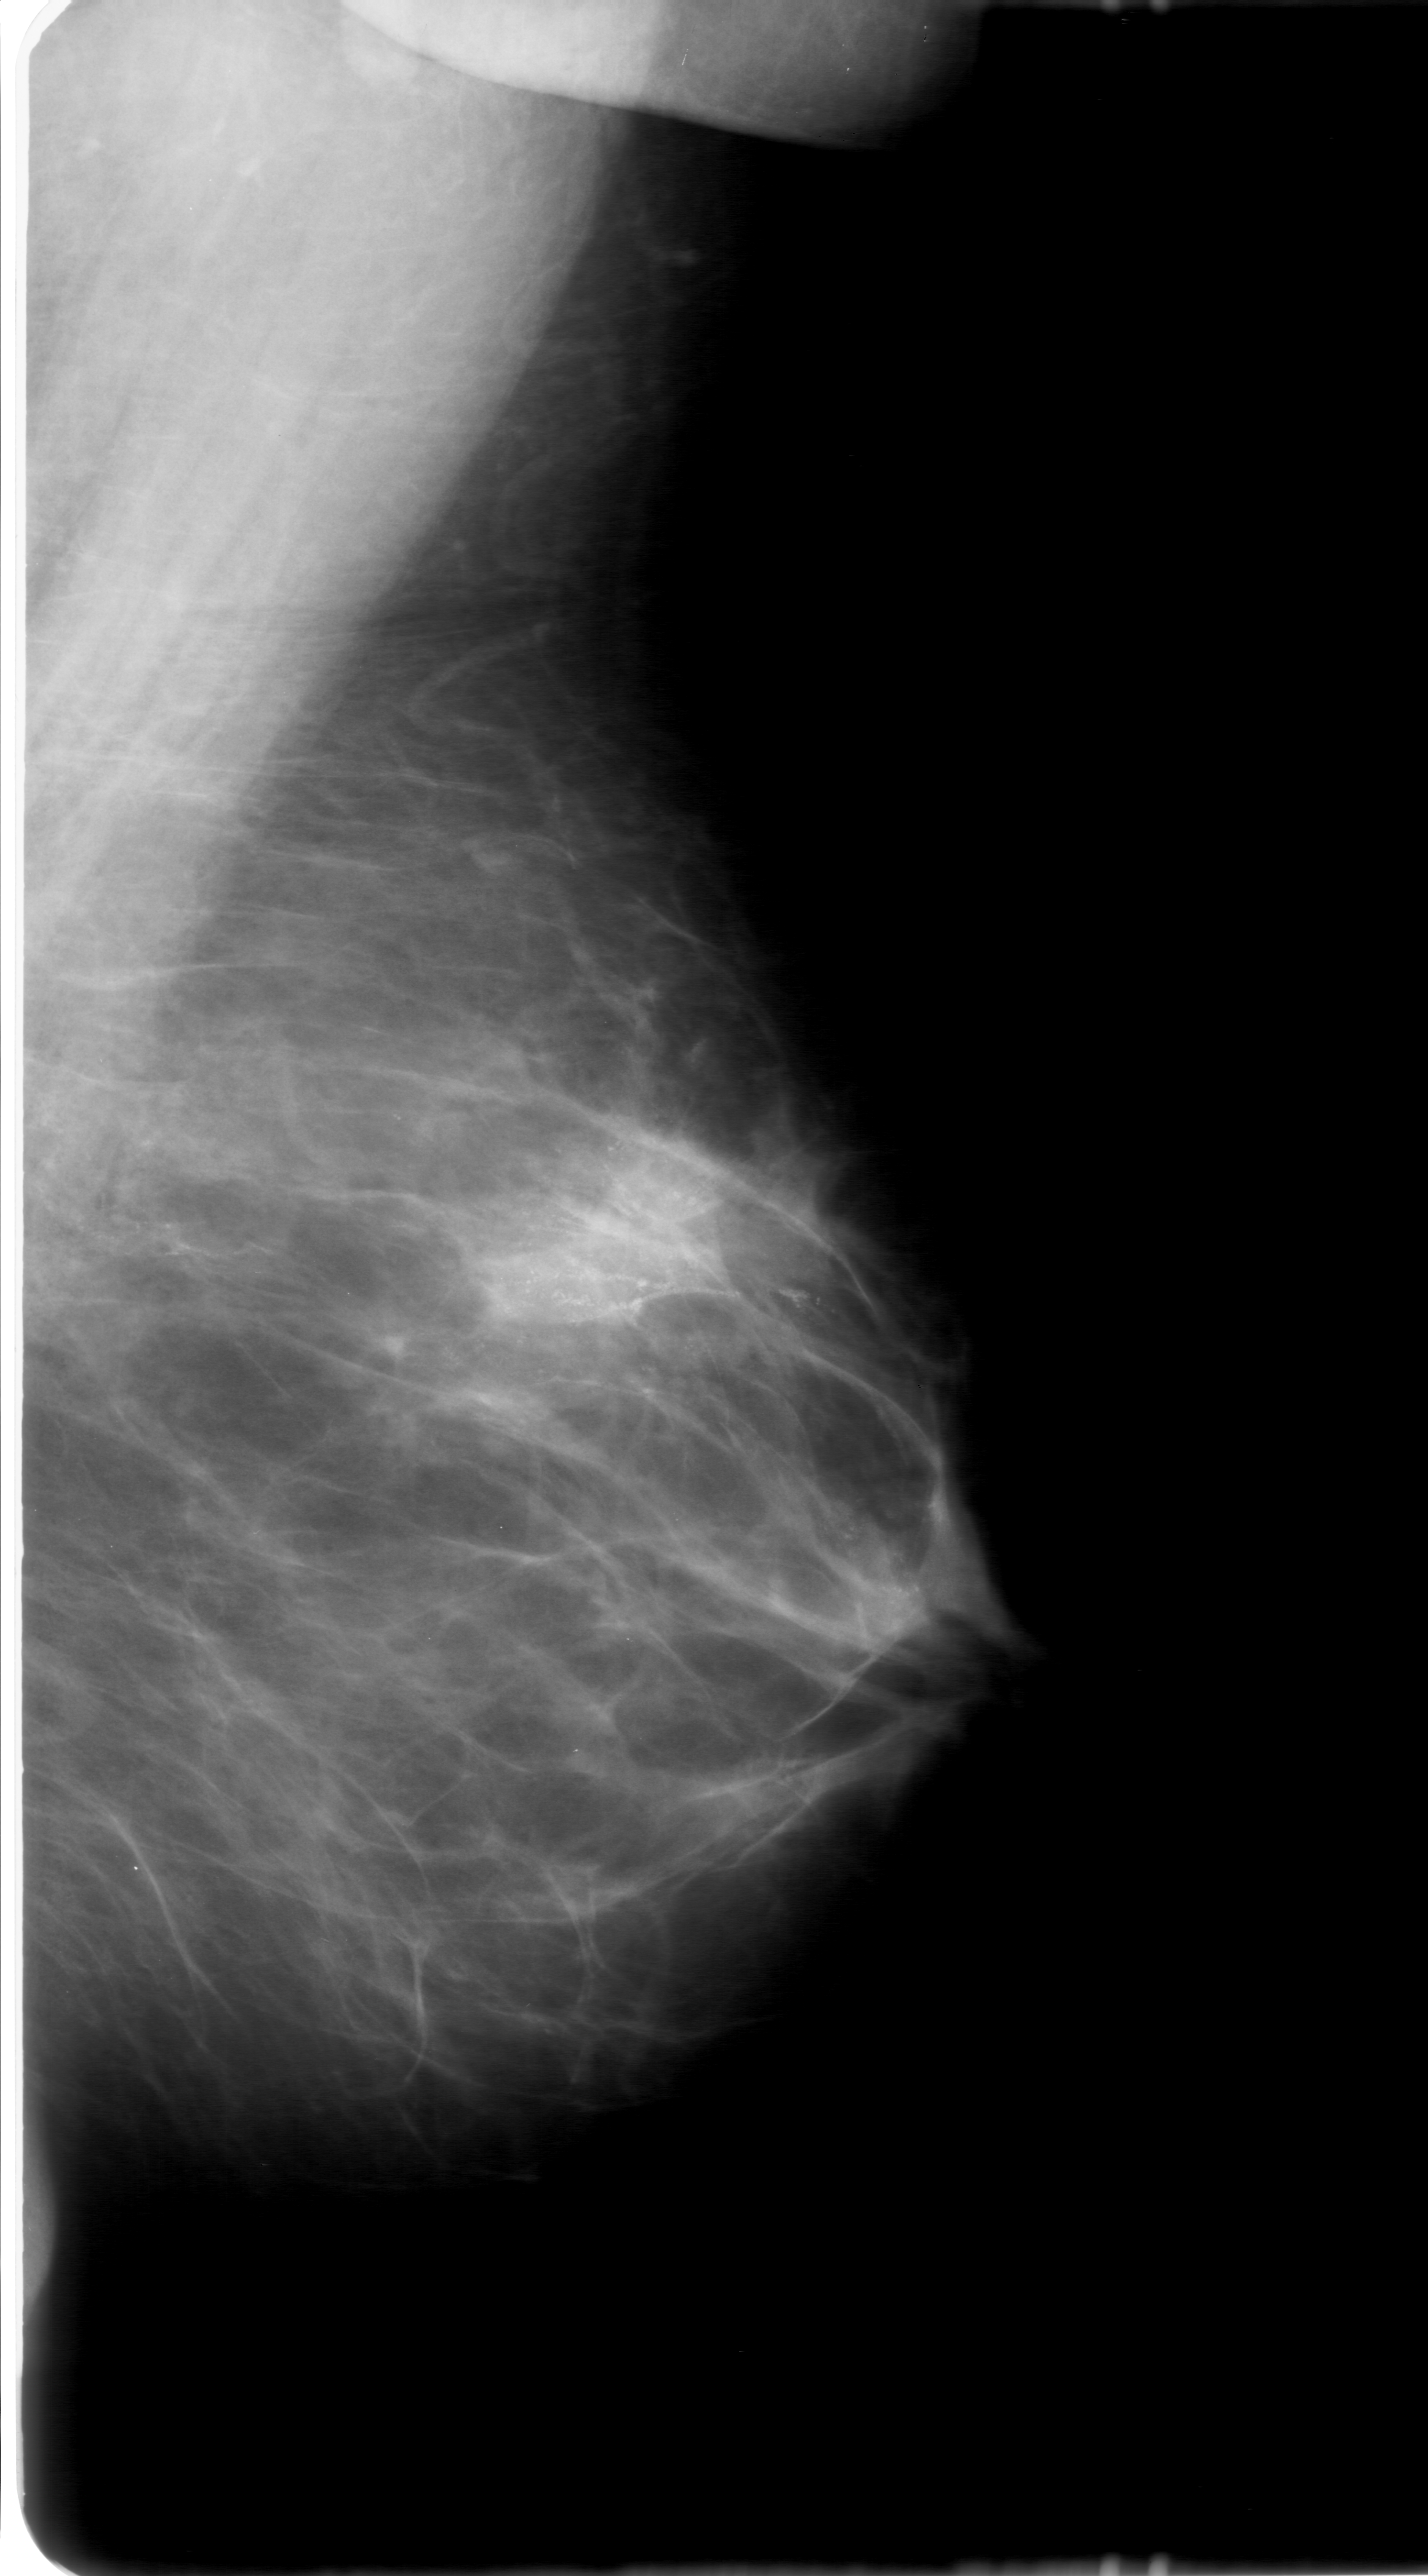
Mammogram (digitized film); left breast; mediolateral oblique (MLO) view; BI-RADS breast density category 2 (scale 1–4); 1428 × 2576 image matrix.
Marked abnormalities (boxes around the expert regions of interest):
- calcifications, morphology amorphous, distribution linear; BI-RADS assessment category 5; subtlety rating 5 on a 1 (subtle) to 5 (obvious) scale; pathology (as recorded): malignant: bounding box [x1, y1, x2, y2] px = [23, 792, 985, 1647]